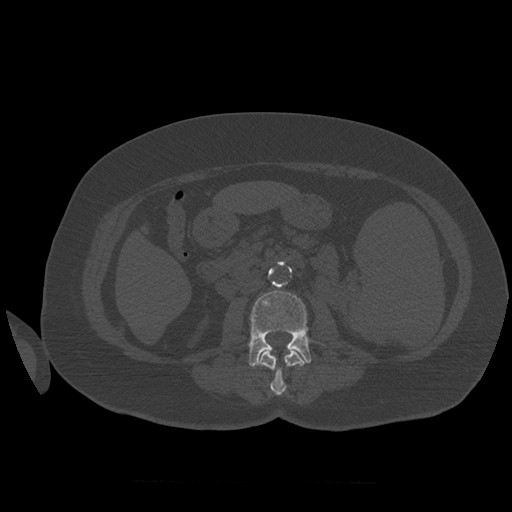
CT including the spine, one axial slice. Slice 238 of 399 in the series (ordered by position). Reconstruction kernel STANDARD. 120 kVp. Bone window (W 1800 / L 400 HU). 1.25 mm slice thickness. 512 × 512 image matrix, field of view 404 × 404 mm. Patient age 81 years. Case-level facts recorded for this patient, not image findings: primary cancer: renal.
Annotated regions visible in this slice (semi-automatic segmentation, software-assisted and operator-edited):
- L2 vertebra: bounding box (x1, y1, x2, y2) in pixels: (256, 349, 307, 396)
- L3 vertebra: (249, 290, 312, 367)